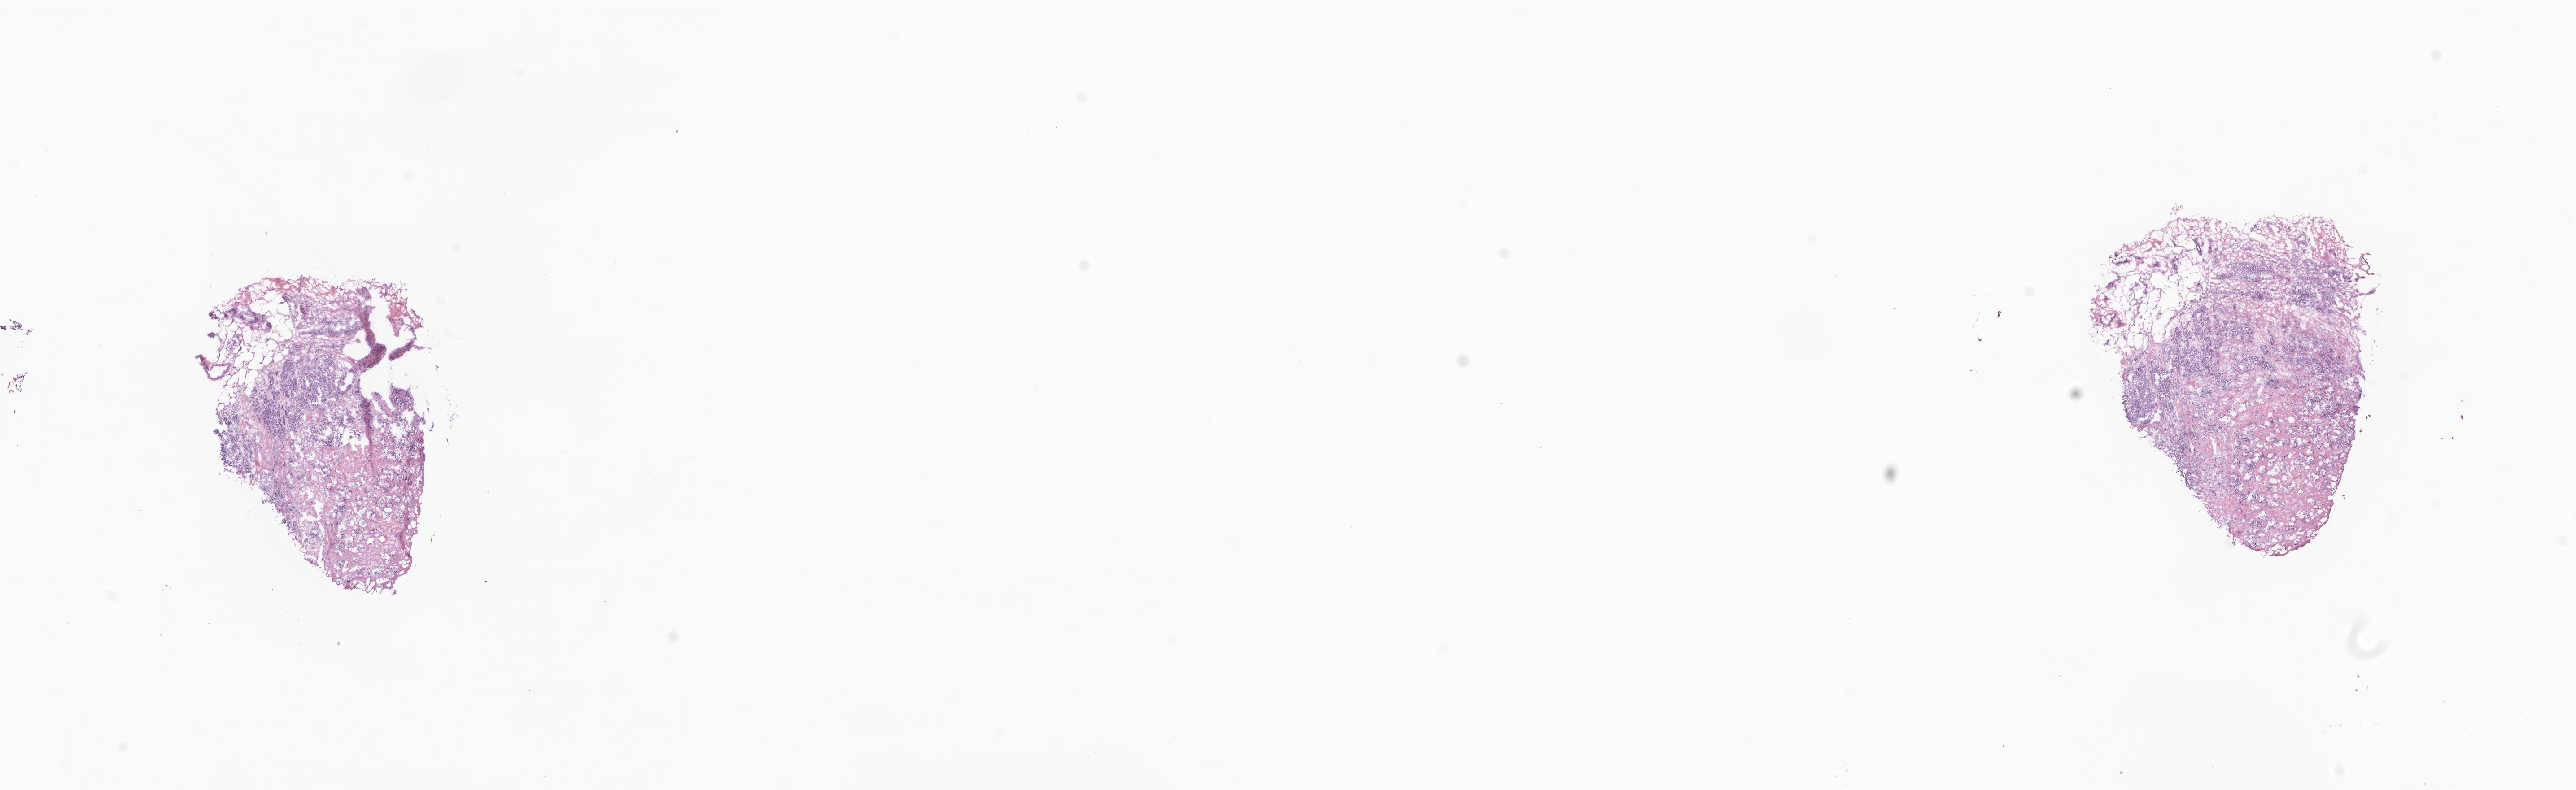
Whole-slide image, hematoxylin and eosin (H&E) stain, shown as a low-resolution overview of the whole scanned area (about 24.2 x 7.4 mm); frozen section (tissue freezing medium); primary tumor; anatomic site: breast. Female patient; age at initial diagnosis 66 years. Slide review estimates, as recorded: tumor cells 30%, tumor nuclei 77%, stromal cells 68%, necrosis 0%, normal cells 2%. Inflammatory infiltration, as recorded: lymphocyte infiltration 18%, monocyte infiltration 1%, neutrophil infiltration 0%.
Histologic diagnosis: Infiltrating duct carcinoma, NOS. Section: bottom of the tissue portion.